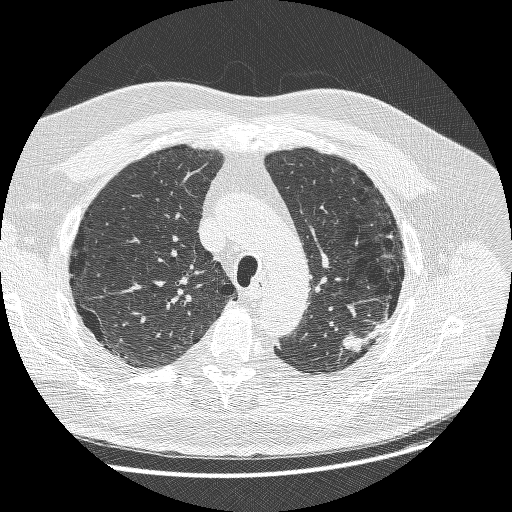
Chest CT (low-dose screening protocol), one axial image. Baseline screening round. Lung window (W 1500 / L -600 HU). 1.25 mm slice thickness. Lung (sharp) reconstruction kernel (BONE). Slice 197 of 258 in the series. 512 × 512 image matrix, field of view 370 × 370 mm. Male participant, aged 68 years at enrolment. Former smoker at enrolment.
Lesion marked by an expert reader, bounding box (x1, y1, x2, y2) in pixels: (334, 311, 390, 362). Screening reader's record for this exam (one nodule recorded; not confirmed to be the boxed lesion): non-calcified nodule or mass ≥4 mm, left upper lobe, 15 × 14 mm, smooth margins, soft tissue attenuation. Lung cancer was diagnosed 19 days after this screen: adenosquamous carcinoma, left upper lobe, poorly differentiated (G3), stage IIIB (AJCC 6th edition), 32 mm at pathology.